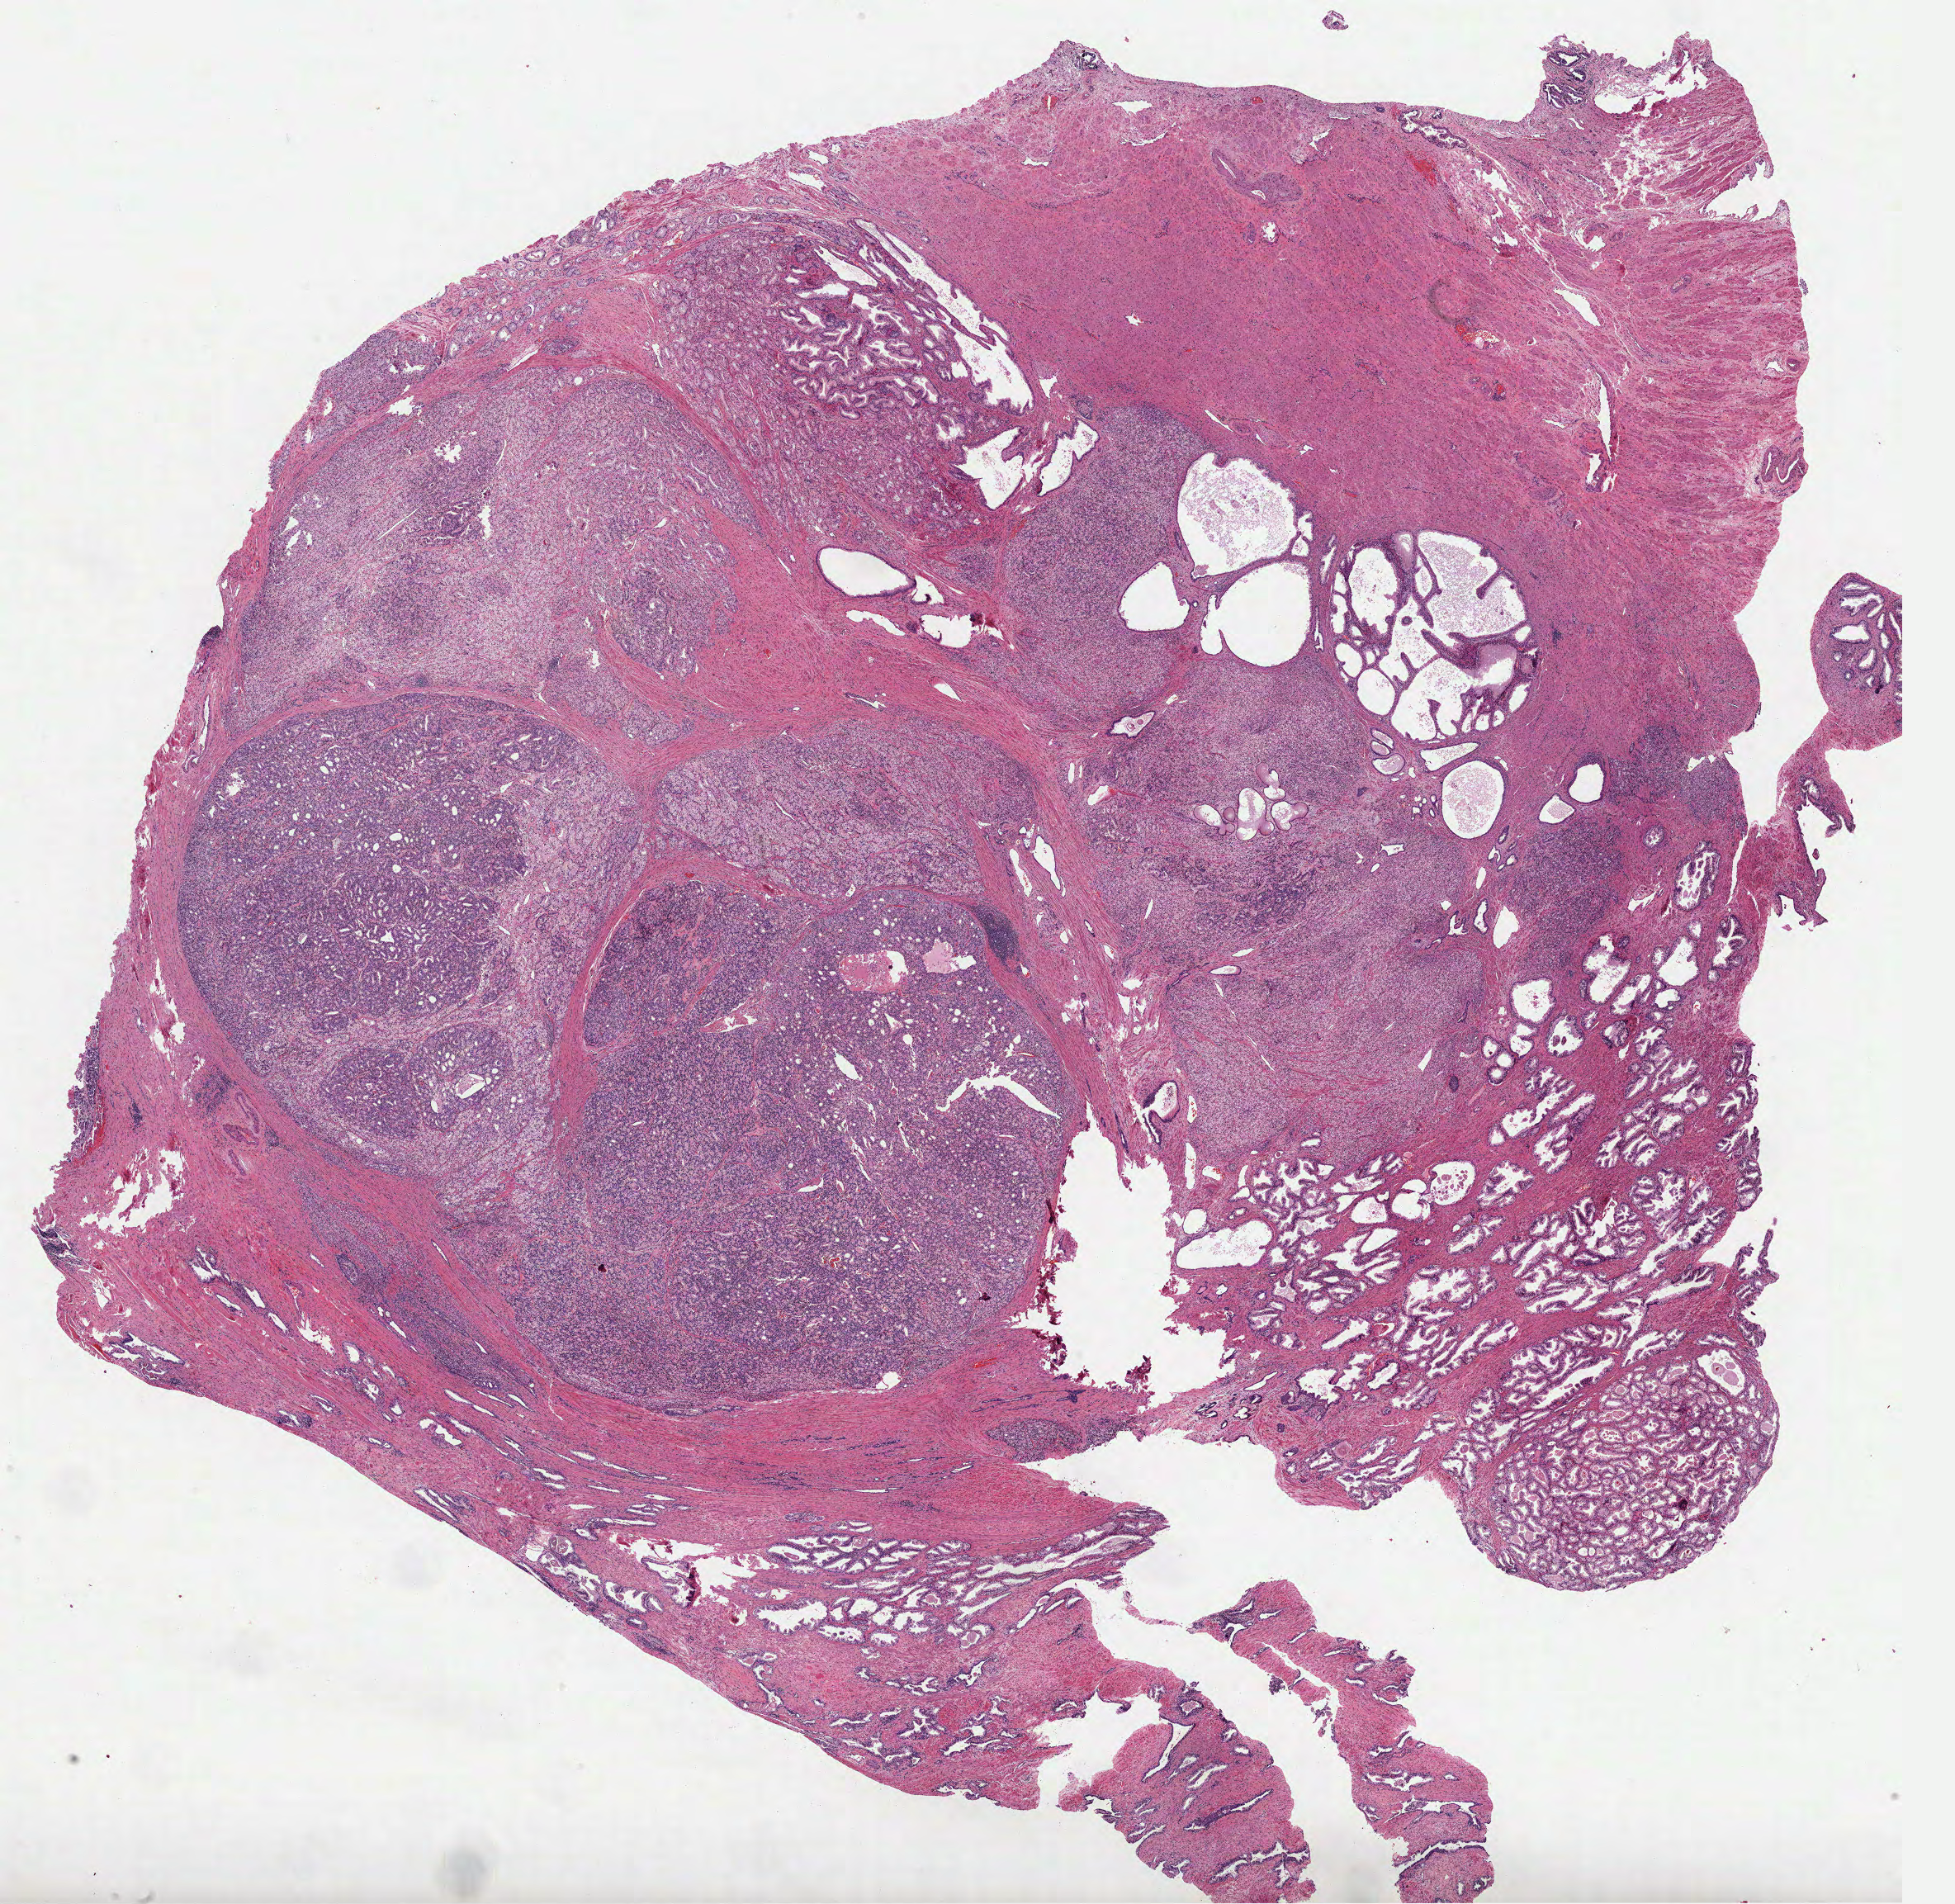
Digitized Hematoxylin and eosin (H&E) stained tissue section (whole slide) — low-resolution overview of the scanned area, about 19.1 x 18.6 mm (slide scanned at 40x), FFPE section, primary tumour sample from the prostate. Patient: male, age at initial diagnosis 66 years.
Diagnosis: Acinar cell carcinoma (prostate gland).